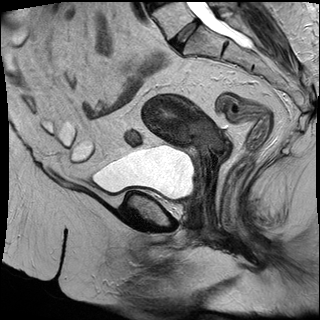
Pelvic MRI for cervical cancer, one sagittal slice. T2-weighted. 1.5 T. TE 87 ms, TR 3063.4 ms. 4 mm slice thickness. 320 × 320 image matrix, field of view 280 × 280 mm. Female patient, age 53 years.
Structures marked on this image (outlined manually by an expert reader):
- uterus and cervix: box from (x=142, y=95) to (x=228, y=153) px